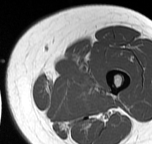
MRI of an extremity soft-tissue mass, one axial slice; position 9 of 57 along the scan axis; MR volume resampled by the dataset authors to the PET/CT grid (not the native acquisition matrix); 152 × 144 image matrix. Female patient. From the clinical record (not read from this slice): histological type: pleiomorphic leiomyosarcoma; grade: intermediate; site of the primary tumour: left thigh.
Structures marked on this image (expert contour drawn on MRI and transferred to this co-registered scan by the dataset authors):
- gross tumour volume including surrounding oedema: bounding box <93,88,99,93> (left, top, right, bottom; pixels)